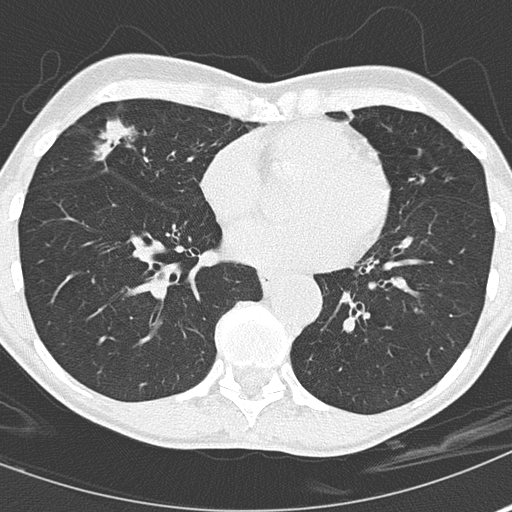
Low-dose screening chest CT, axial slice. Second annual screen. Lung window (W 1500 / L -600 HU). 2 mm slice thickness. Slice 105 of 167 in the series. Female, age 67 years at enrolment. Current smoker at enrolment.
Lesion marked by an expert reader, bounding box <83,111,188,201> (left, top, right, bottom; pixels). The screening reader recorded 2 non-calcified nodules or masses ≥4 mm on this exam (right middle lobe, right middle lobe); which of them this box marks is not recorded. Official screen result: positive, other. Lung cancer was diagnosed 475 days after this screen (after the third annual screen): bronchiolo-alveolar adenocarcinoma, NOS, right middle lobe, well differentiated (G1), stage IA (AJCC 6th edition), 25 mm at pathology.